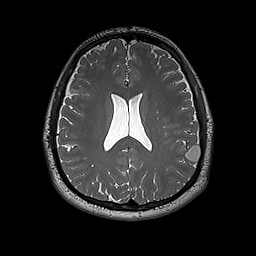
Brain MRI from a brain-tumour surgery series, one axial slice. Position 81 of 192 along the scan axis. 1 mm slice thickness. 256 × 256 image matrix, field of view 250 × 250 mm. From the clinical record (not read from this slice): histopathology: Dysembryoplastic neuroepithelial tumor; WHO grade: 1; IDH mutation: no; tumour location: Left Inferior Parietal.
Annotated regions visible in this slice (outlined manually by an expert reader):
- tumour: bounding box [x1, y1, x2, y2] px = [185, 146, 201, 162]